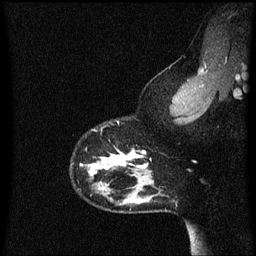
Breast MRI (dynamic contrast-enhanced), one sagittal slice. Position 49 of 60 along the scan axis. Dynamic contrast-enhanced series, image 2 of 3 at this slice position (ordered by acquisition). 1.5 T. TE 4.2 ms, TR 8.4 ms. 2 mm slice thickness. 256 × 256 image matrix, field of view 200 × 200 mm. Female patient, age 33 years.
Structures marked on this image (semi-automatically segmented with operator editing):
- analysis volume of interest (the breast-tissue region the enhancement analysis was run in; not a lesion): bounding box <72,148,152,191> (left, top, right, bottom; pixels)
- tumour enhancement mask (voxels above the 70 % enhancement threshold inside the analysis volume of interest): <81,150,148,175>